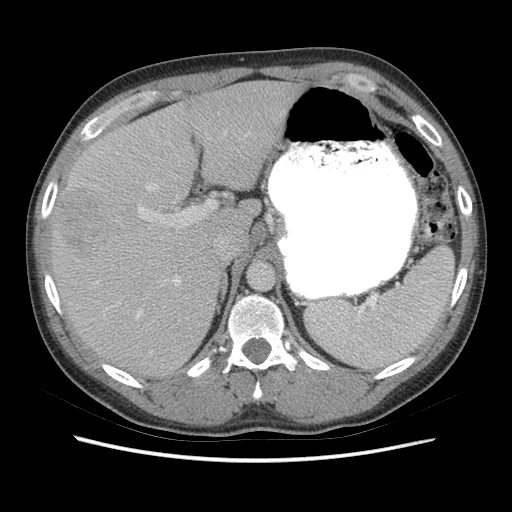
Contrast-enhanced abdominal CT (liver protocol), one axial slice. Position 46 of 73 along the scan axis. Reconstruction kernel STANDARD. 140 kVp. Soft-tissue window (W 400 / L 40 HU). 2.5 mm slice thickness. 512 × 512 image matrix. Case-level facts recorded for this patient, not image findings: diagnosis: hepatocellular carcinoma (patient treated with transarterial chemoembolisation; whether this scan precedes or follows treatment is not stated here); TNM stage (as recorded): Stage-IIIA.
Annotated regions visible in this slice (semi-automatic segmentation, software-assisted and operator-edited):
- liver parenchyma outside the tumour (the mass and vessels are separate outlines, so this box may not span the whole liver): bounding box [x1, y1, x2, y2] px = [50, 80, 300, 376]
- mass: [58, 189, 100, 259]
- liver vessels: [95, 132, 226, 318]